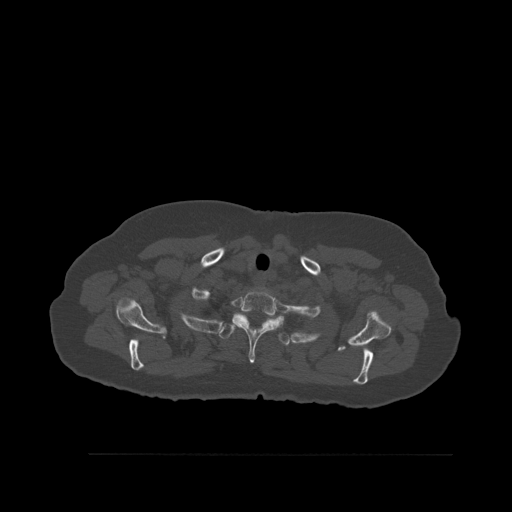
CT including the spine, one axial slice; slice 440 of 527 in the series (ordered by position); bone window (W 1800 / L 400 HU); 1.5 mm slice thickness; 512 × 512 image matrix, field of view 470 × 470 mm. Female patient, age 73 years. Case-level facts recorded for this patient, not image findings: primary cancer: breast.
Structures marked on this image (semi-automatic segmentation, software-assisted and operator-edited):
- T1 vertebra: box from (x=234, y=288) to (x=284, y=363) px
- T2 vertebra: (x=219, y=316)–(x=290, y=346)